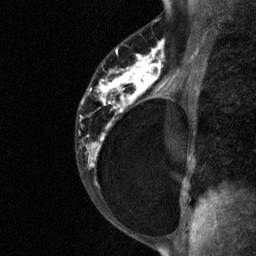
Breast MRI (dynamic contrast-enhanced), one sagittal slice; position 42 of 64 along the scan axis; dynamic contrast-enhanced study with each time point stored as its own series, time point 2 of 3 at this slice position (early post-contrast, ordered by acquisition time); 1.5 T; TE 4.8 ms, TR 27 ms; 2 mm slice thickness; 256 × 256 image matrix. Female patient, age 34 years. From the clinical record (not read from this slice): setting: breast cancer imaged before/during neoadjuvant chemotherapy; receptor status: HR-positive, HER2-negative.
Structures marked on this image (semi-automatic segmentation, software-assisted and operator-edited):
- analysis volume of interest (the breast-tissue region the enhancement analysis was run in; not a lesion): bounding box <78,44,181,191> (left, top, right, bottom; pixels)
- tumour enhancement mask (voxels above the 90 % enhancement threshold inside the analysis volume of interest): <82,44,164,167>